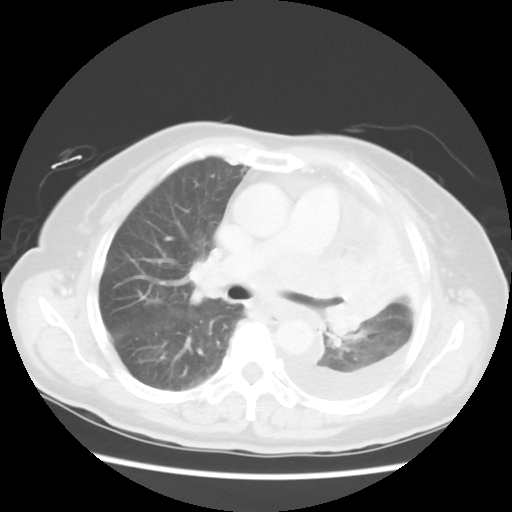
Chest CT, one axial slice; position 33 of 52 along the scan axis; 120 kVp; lung window (W 1500 / L -600 HU); 512 × 512 image matrix, field of view 336 × 336 mm. Female patient, age 72 years. Case-level facts recorded for this patient, not image findings: clinical TNM (as recorded): T4 N3 M1b; histopathological grade: G3.
Outlined on this slice (rectangle marked by the reading radiologist):
- lung tumour (recorded histology: large cell carcinoma): bounding box <305,246,396,350> (left, top, right, bottom; pixels)